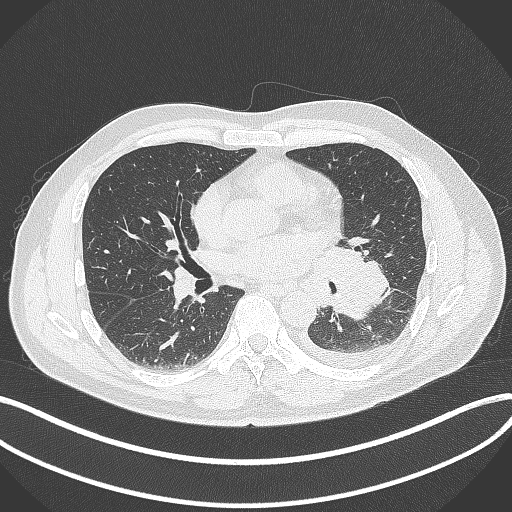
Chest CT, one axial slice; lung window (W 1500 / L -600 HU); 512 × 512 image matrix, field of view 400 × 400 mm. Male patient, age 58 years. Case-level facts recorded for this patient, not image findings: clinical TNM (as recorded): T3 N1 M1b; histopathological grade: G3.
Structures marked on this image (rectangle marked by the reading radiologist):
- lung tumour (recorded histology: small cell carcinoma): box from (x=311, y=236) to (x=396, y=323) px